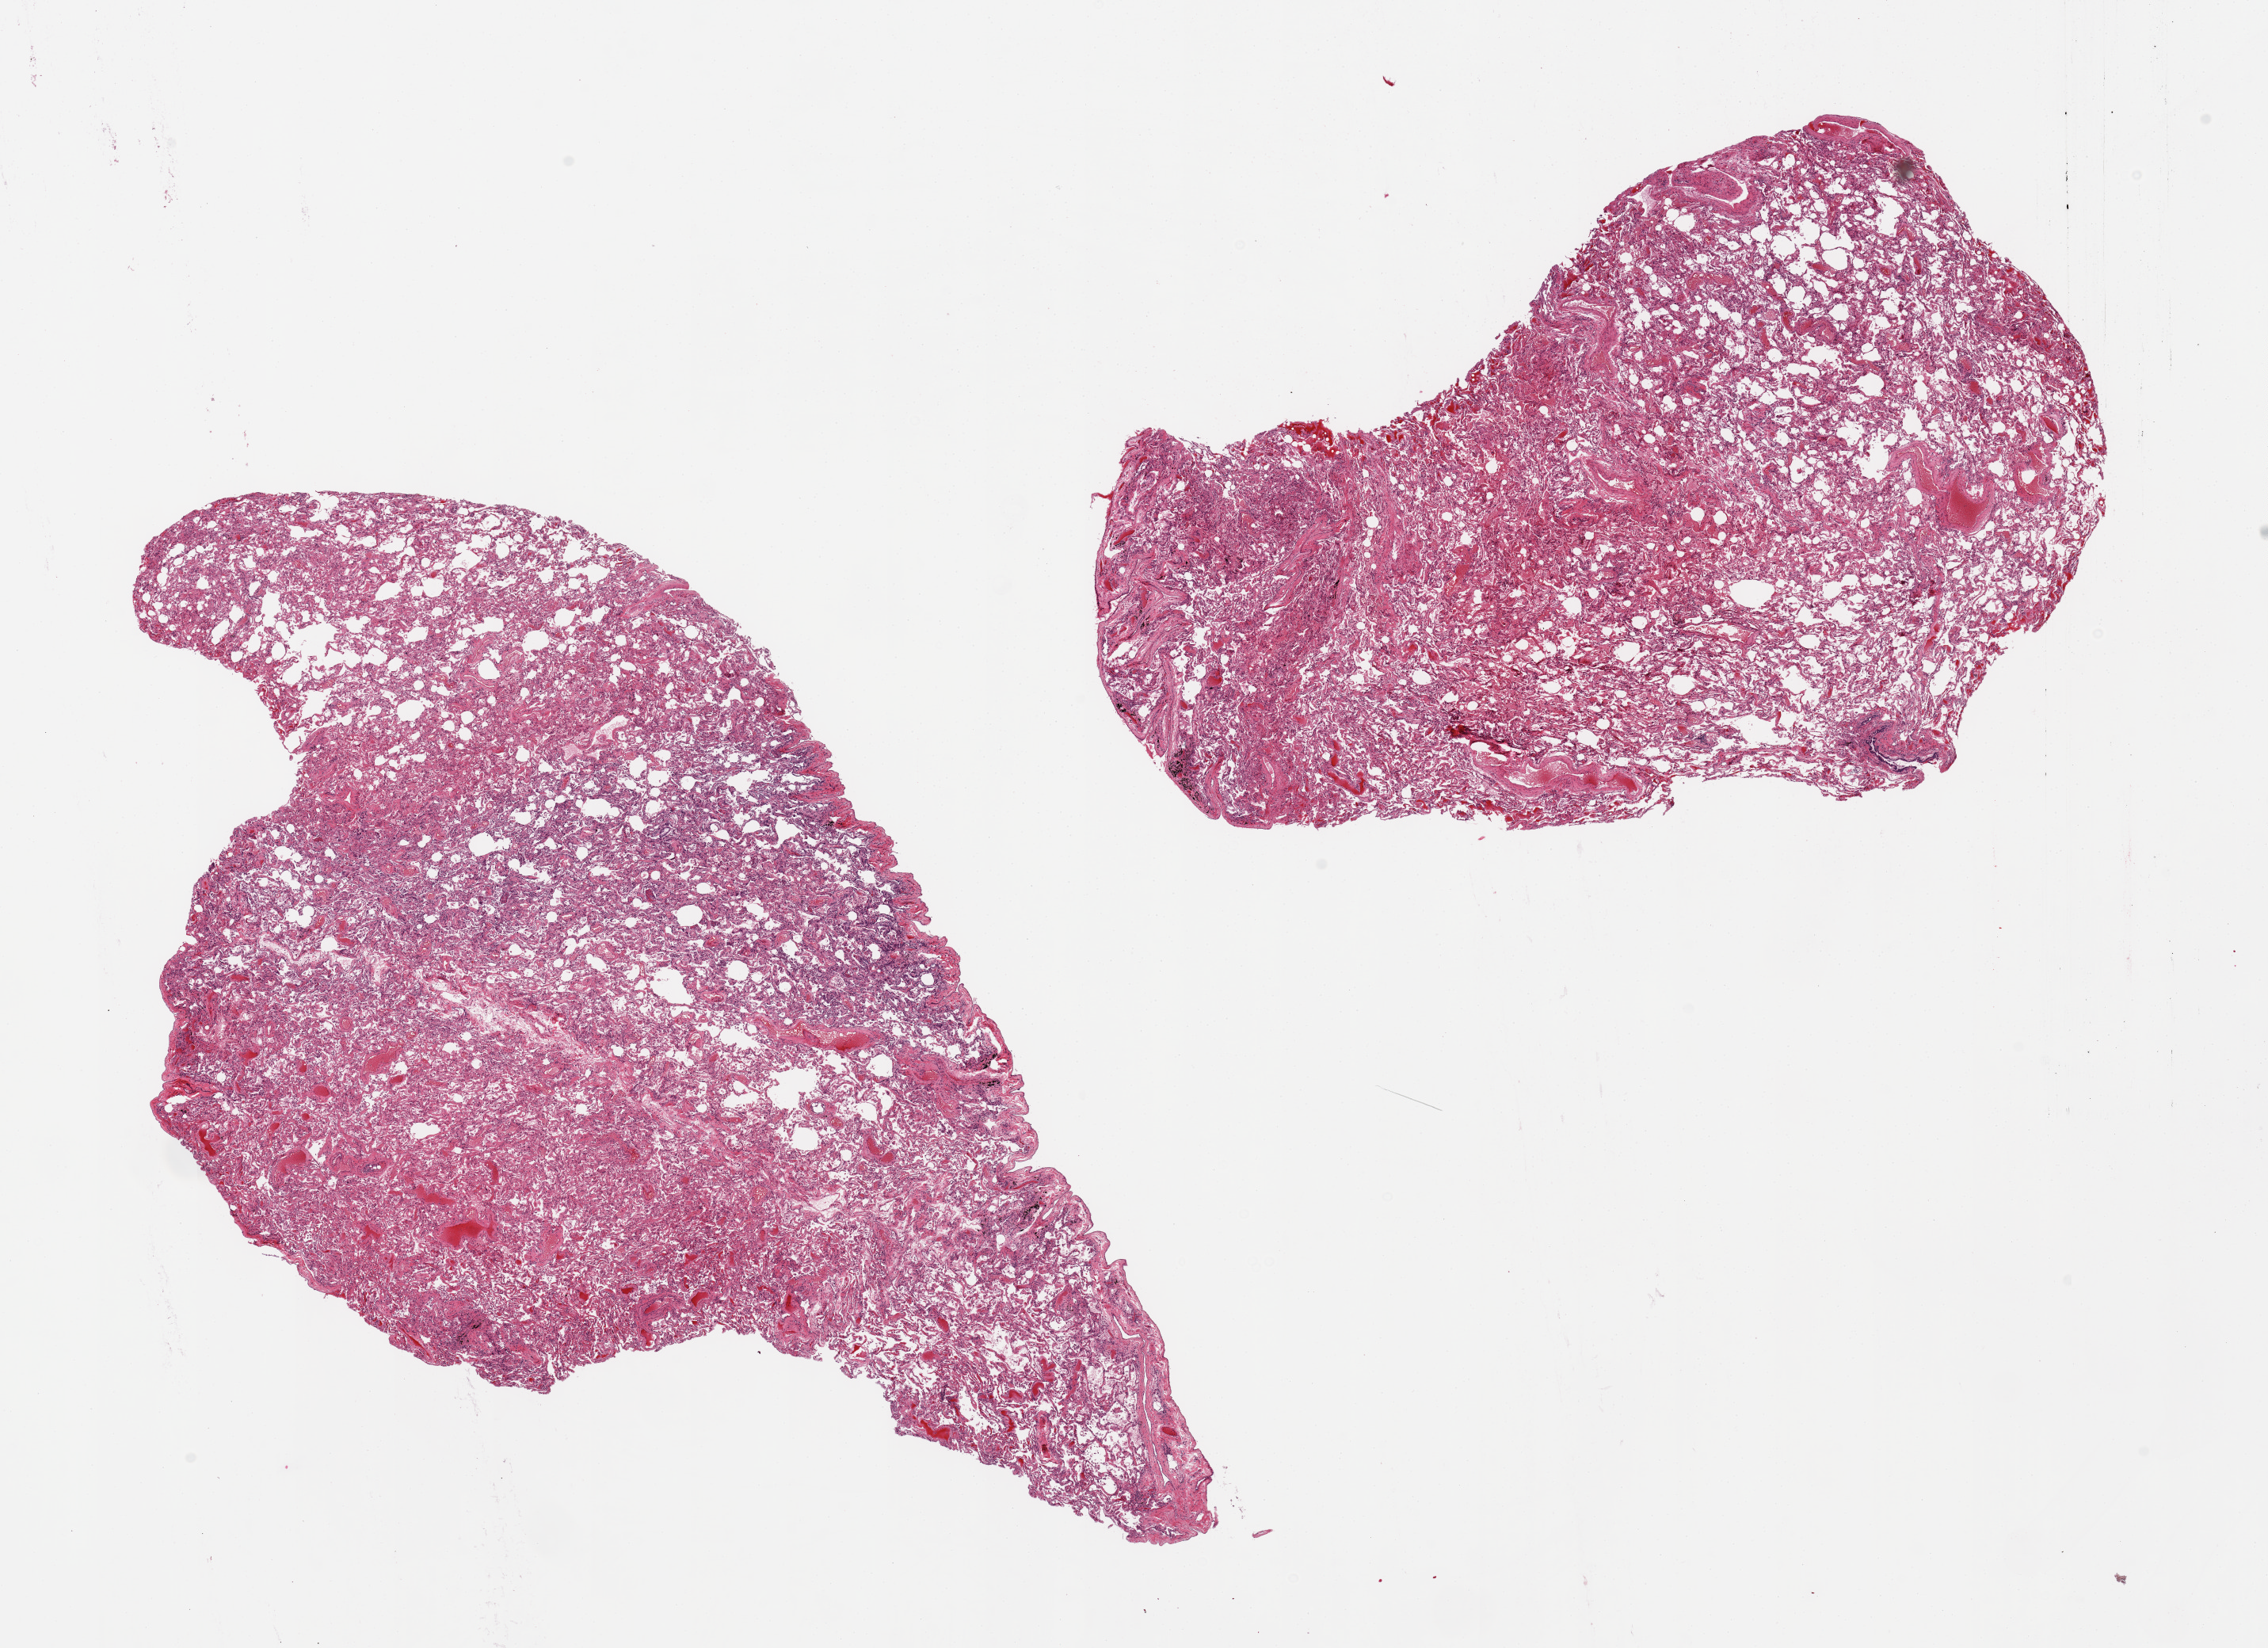
H&E whole-slide image, brightfield — whole scanned area (about 22.6 x 16.4 mm, from a 20x scan) shown as a low-resolution overview. PAXgene-fixed, paraffin-embedded tissue. Section of lung (target tissue). Tissue donor sample. Donor: male.
- reviewer comment on this tissue sample: 2 pieces, mild congestion